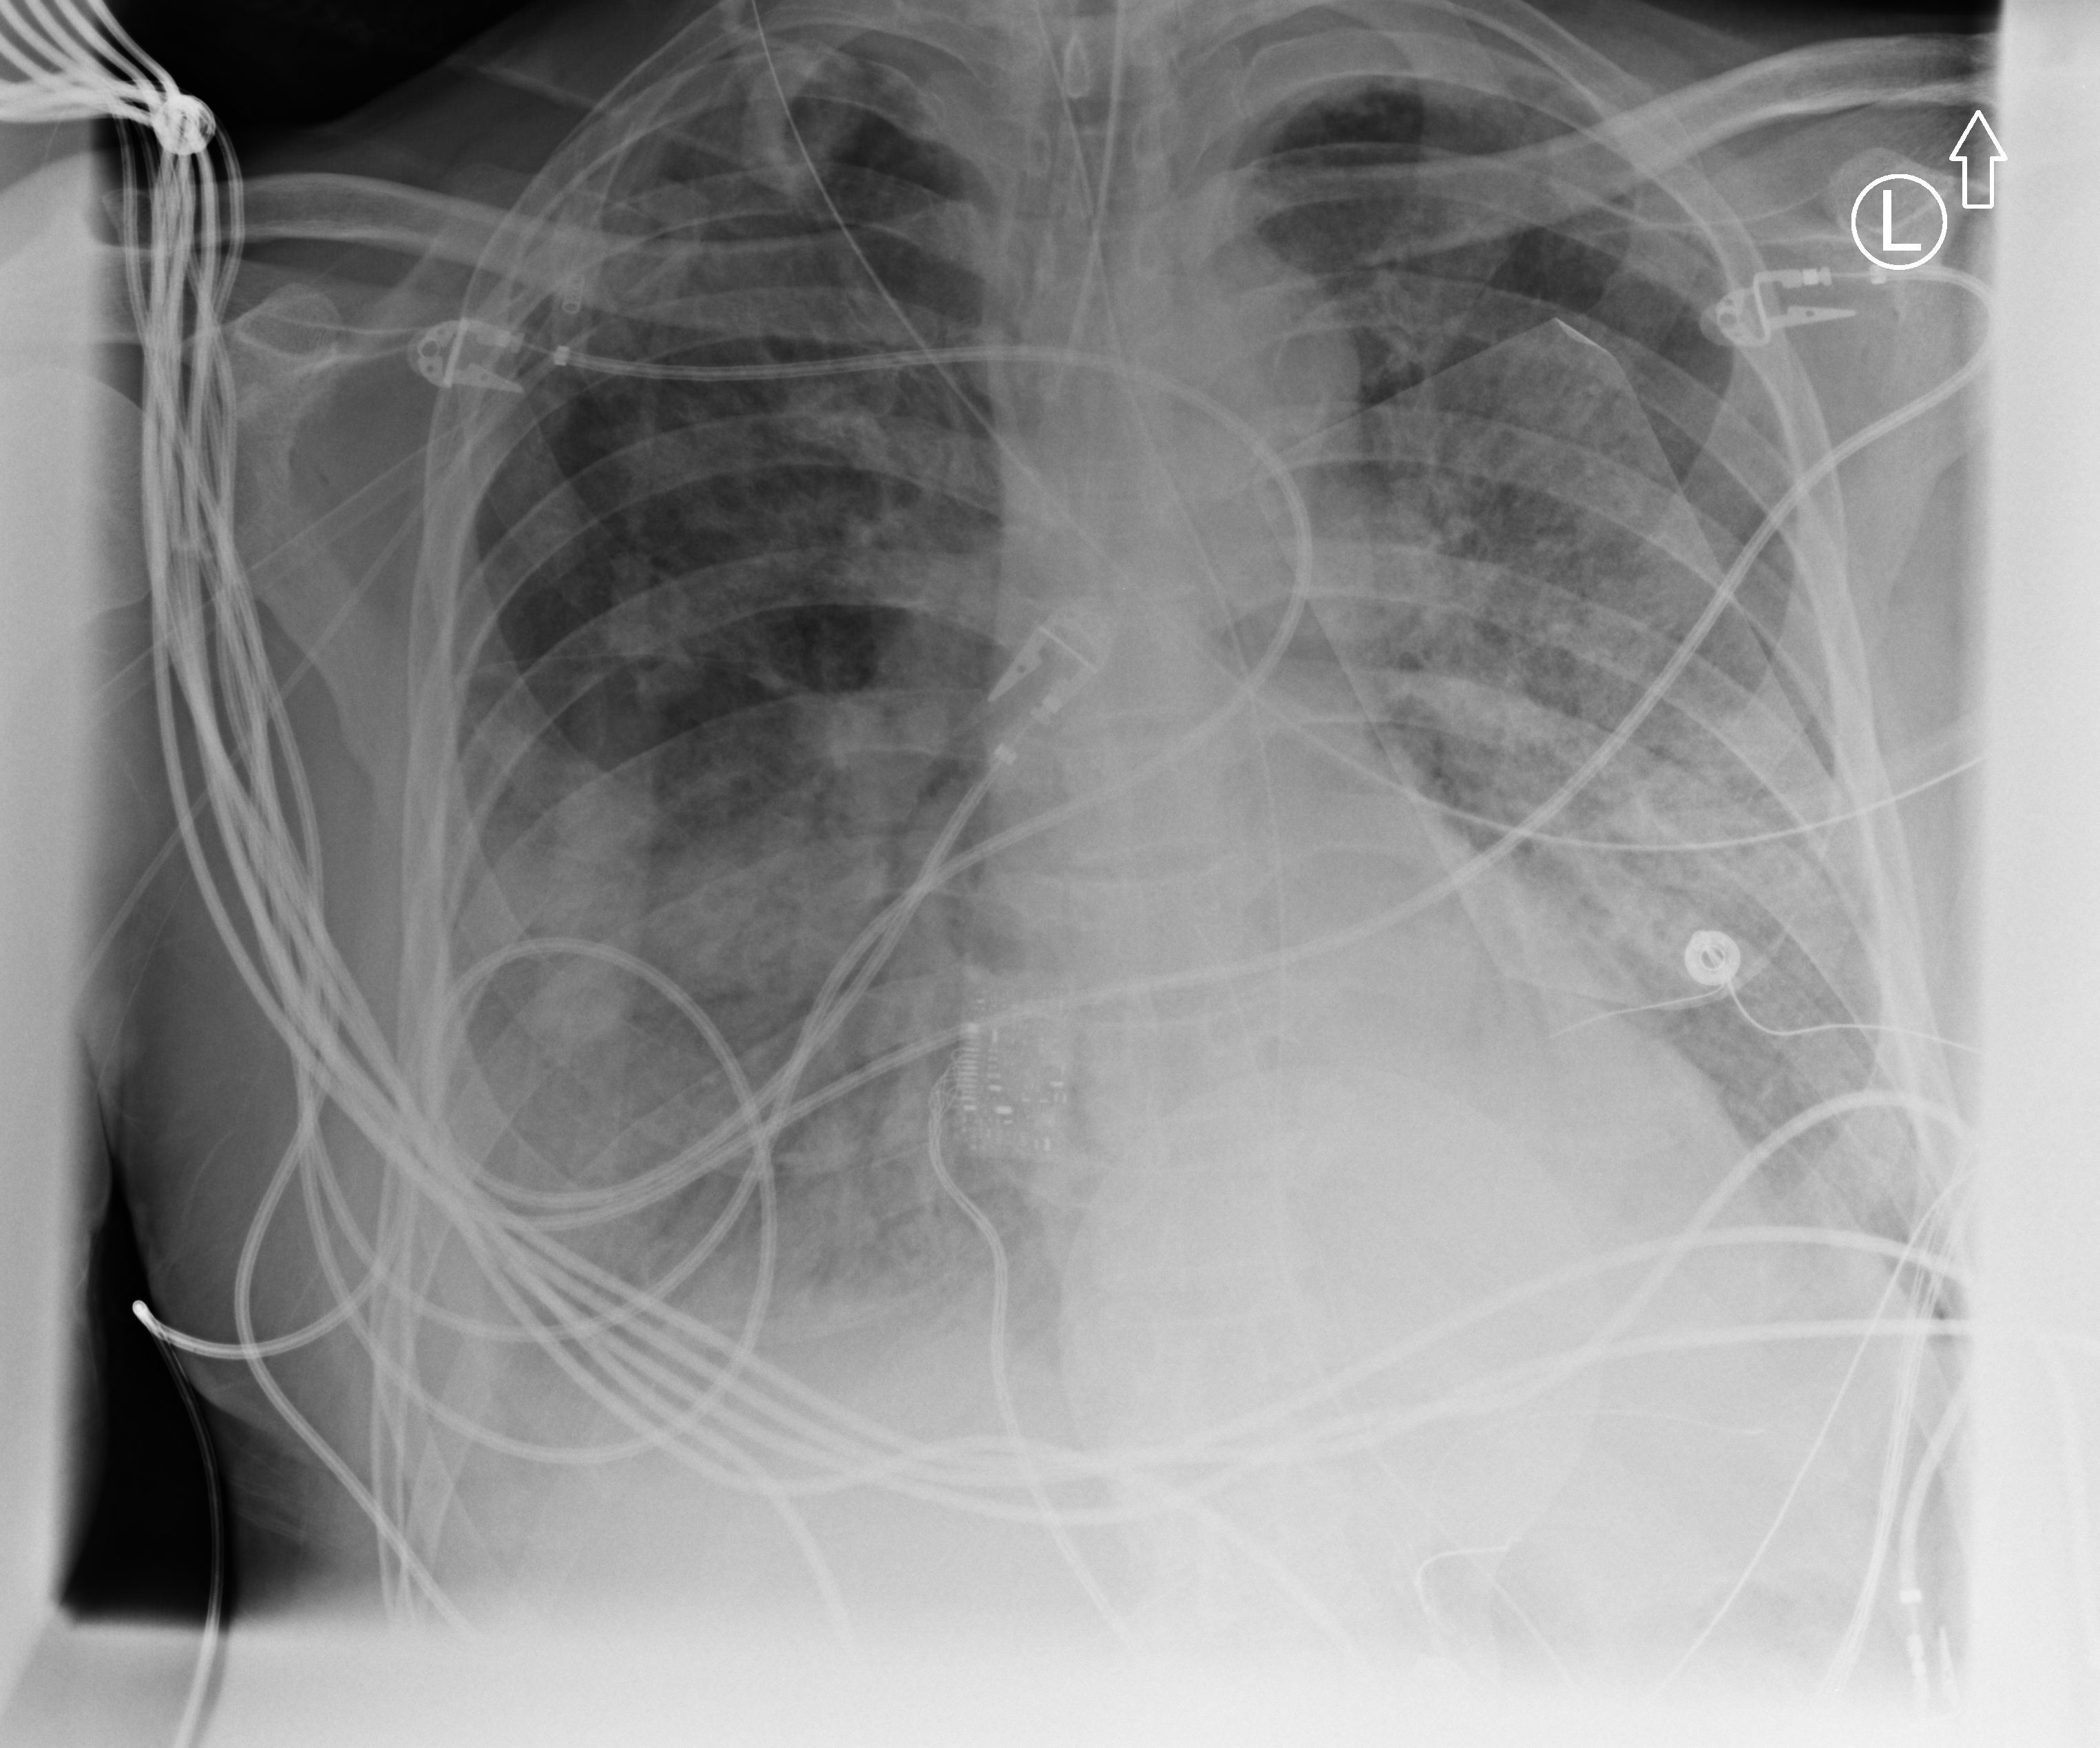
Portable chest radiograph, anteroposterior (AP) projection. Male patient hospitalised with COVID-19, age 60–74 years.
Hospital-stay facts (about this admission, not read from this image; timing relative to this image not recorded): mechanically ventilated during this hospital stay: yes; admitted to intensive care during this hospital stay: yes; other chronic lung disease (admission record): no.